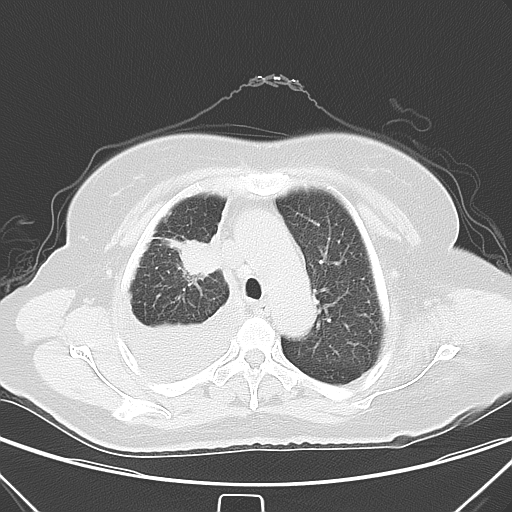
Chest CT, one axial slice. Slice 43 of 55 in the series (ordered by position). Lung window (W 1500 / L -600 HU). 5 mm slice thickness. 512 × 512 image matrix, field of view 352 × 352 mm. Female patient, age 66 years. From the clinical record (not read from this slice): clinical TNM (as recorded): T2 N0 M1.
Outlined on this slice (bounding box drawn by a radiologist):
- lung tumour (recorded histology: adenocarcinoma): bounding box (x1, y1, x2, y2) in pixels: (173, 232, 221, 280)